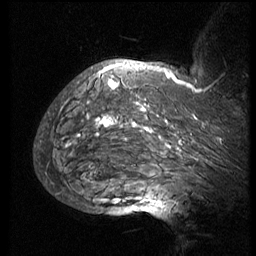
Breast MRI (dynamic contrast-enhanced), one sagittal slice; 3 images stored at this slice position (order not interpretable as contrast timing); 1.5 T; TE 4.2 ms, TR 8.9 ms; 2.5 mm slice thickness; 256 × 256 image matrix, field of view 200 × 200 mm. Patient: female, 57 years. Case-level facts recorded for this patient, not image findings: setting: breast cancer imaged before/during neoadjuvant chemotherapy; receptor status: HER2-positive.
Structures marked on this image (semi-automatic segmentation, software-assisted and operator-edited):
- analysis volume of interest (the breast-tissue region the enhancement analysis was run in; not a lesion): bounding box [x1, y1, x2, y2] px = [51, 67, 247, 173]
- tumour enhancement mask (voxels above the 140 % enhancement threshold inside the analysis volume of interest): [63, 67, 201, 148]